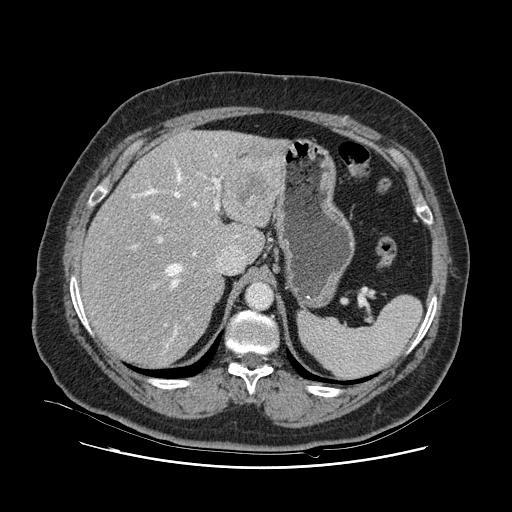
Contrast-enhanced abdominal CT, one axial slice; position 81 of 132 along the scan axis; intravenous contrast given; soft-tissue window (W 400 / L 40 HU); 512 × 512 image matrix. Female patient, age 73 years. Case-level facts recorded for this patient, not image findings: diagnosis: colorectal cancer liver metastases, imaged before liver resection; multiple liver metastases: no; largest metastasis: 7 cm.
Outlined on this slice (manually delineated by an expert):
- hepatic veins: bounding box <132,154,238,348> (left, top, right, bottom; pixels)
- liver: <83,131,281,365>
- planned liver remnant (the part of the liver to remain after resection): <83,160,238,365>
- portal vein (with intrahepatic branches): <130,172,222,326>
- liver metastasis: <235,161,271,205>